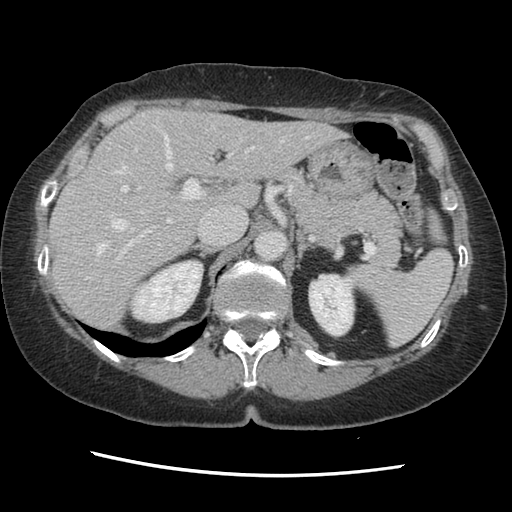
Contrast-enhanced abdominal CT, one axial slice. Slice 91 of 141 in the series (ordered by position). Soft-tissue window (W 400 / L 40 HU). 2.5 mm slice thickness. 512 × 512 image matrix, field of view 330 × 330 mm. Female patient, age 61 years. From the clinical record (not read from this slice): diagnosis: colorectal cancer liver metastases, imaged before liver resection; multiple liver metastases: no; largest metastasis: 2.4 cm; chemotherapy before resection: no.
Structures marked on this image (manually delineated by an expert):
- hepatic veins: bounding box [x1, y1, x2, y2] px = [88, 128, 310, 279]
- liver: [50, 110, 341, 332]
- planned liver remnant (the part of the liver to remain after resection): [50, 110, 341, 332]
- portal vein (with intrahepatic branches): [117, 148, 231, 261]